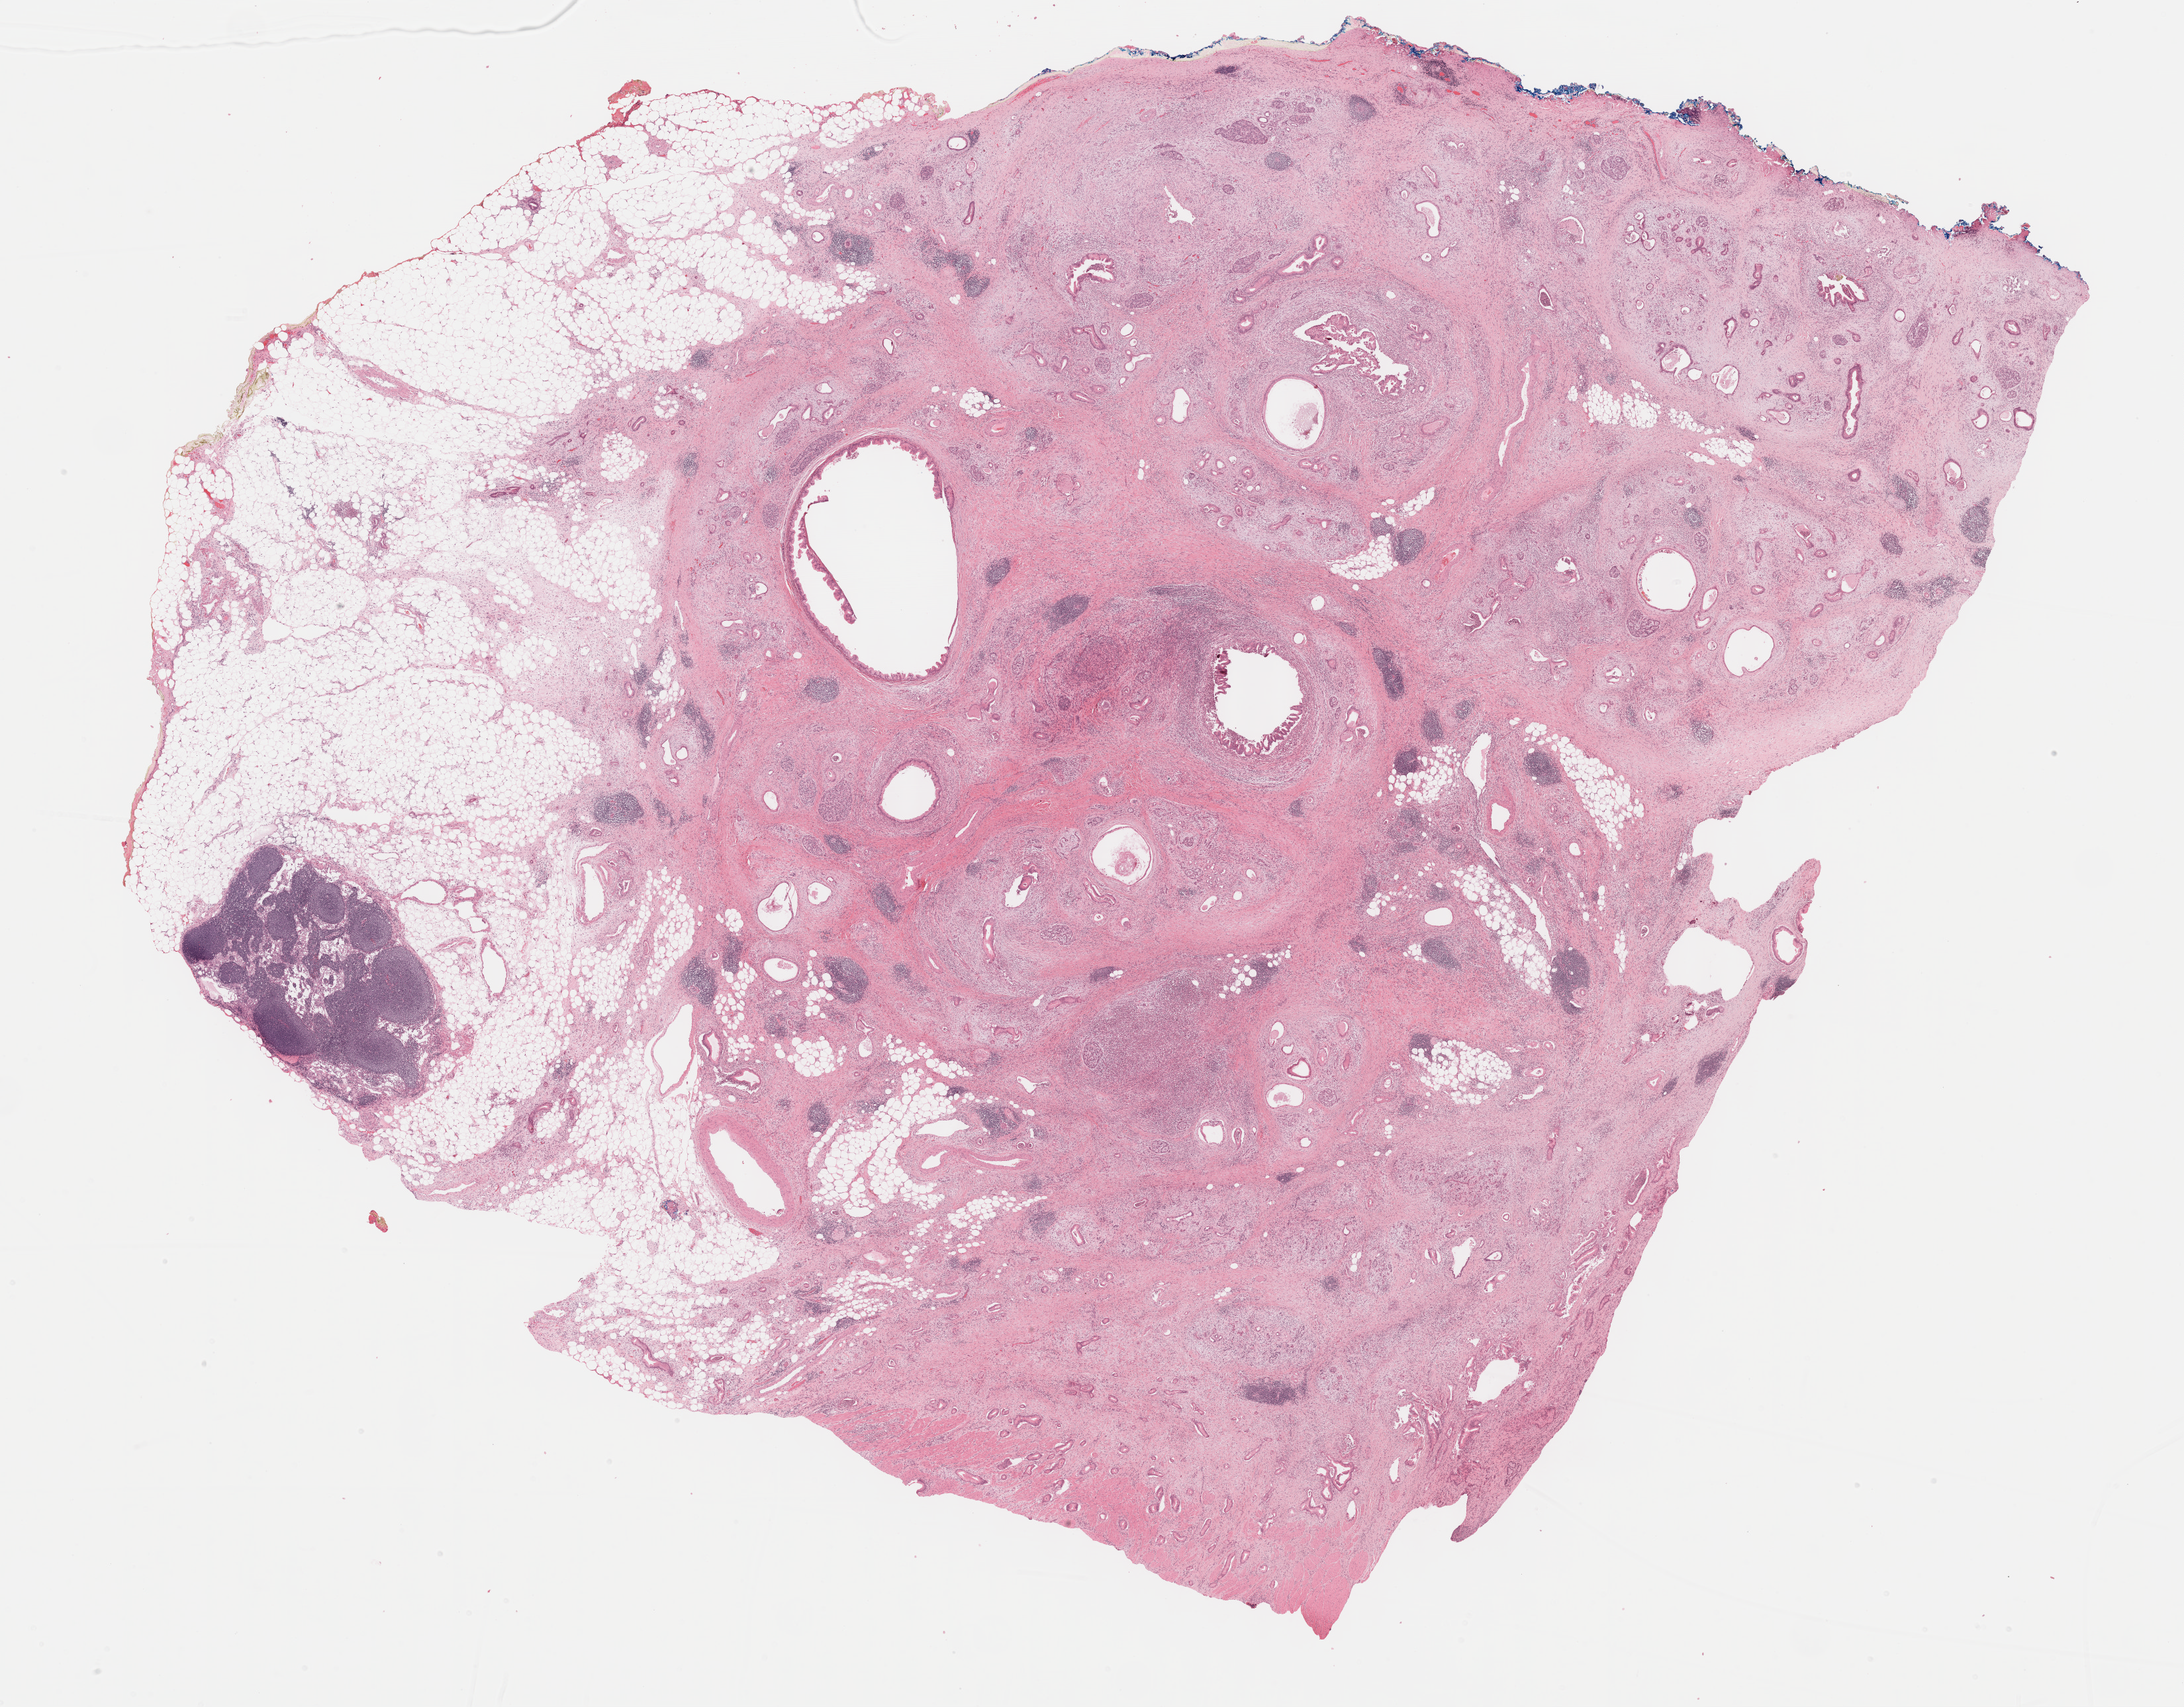
Digitized Hematoxylin and eosin (H&E) stained tissue section (whole slide), shown as a low-resolution overview of the whole scanned area (about 26.7 x 20.9 mm), FFPE section, sample: primary tumour, pancreas. Female patient; age at initial diagnosis 66 years. Histologic grade: G2 (moderately differentiated).
- diagnosis: Infiltrating duct carcinoma, NOS
- lymph nodes positive (case pathology): 0 of 12 examined
- AJCC pathologic stage: IIA (6th edition)